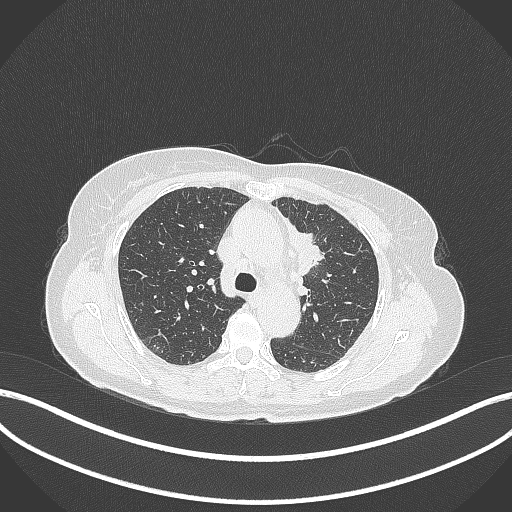
Chest CT, one axial slice; slice 232 of 369 in the series (ordered by position); reconstruction kernel B70f; 120 kVp; lung window (W 1500 / L -600 HU); 512 × 512 image matrix, field of view 400 × 400 mm. Female patient, age 65 years. Case-level facts recorded for this patient, not image findings: clinical TNM (as recorded): T2a N0 M0.
Annotated regions visible in this slice (bounding box drawn by a radiologist):
- lung tumour (recorded histology: adenocarcinoma): box from (x=281, y=217) to (x=328, y=279) px